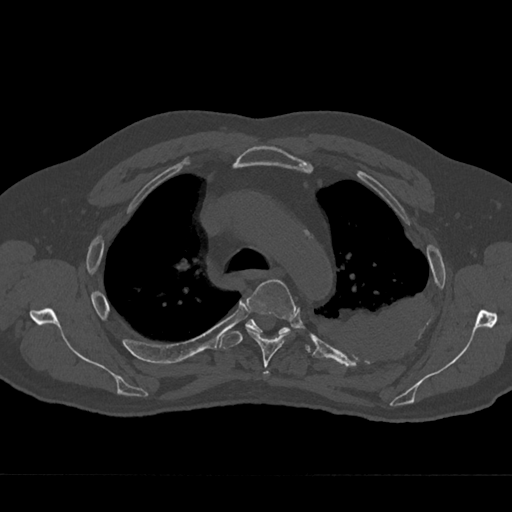
CT including the spine, one axial slice; position 505 of 797 along the scan axis; 120 kVp; bone window (W 1800 / L 400 HU); 0.5 mm slice thickness; 512 × 512 image matrix, field of view 377 × 377 mm. Male patient, age 75 years. From the clinical record (not read from this slice): primary cancer: renal; vertebrae with lytic lesions (as recorded): T4.
Structures marked on this image (semi-automatic segmentation, software-assisted and operator-edited):
- T4 vertebra: bounding box [x1, y1, x2, y2] px = [246, 279, 295, 376]
- T5 vertebra: [219, 319, 311, 352]